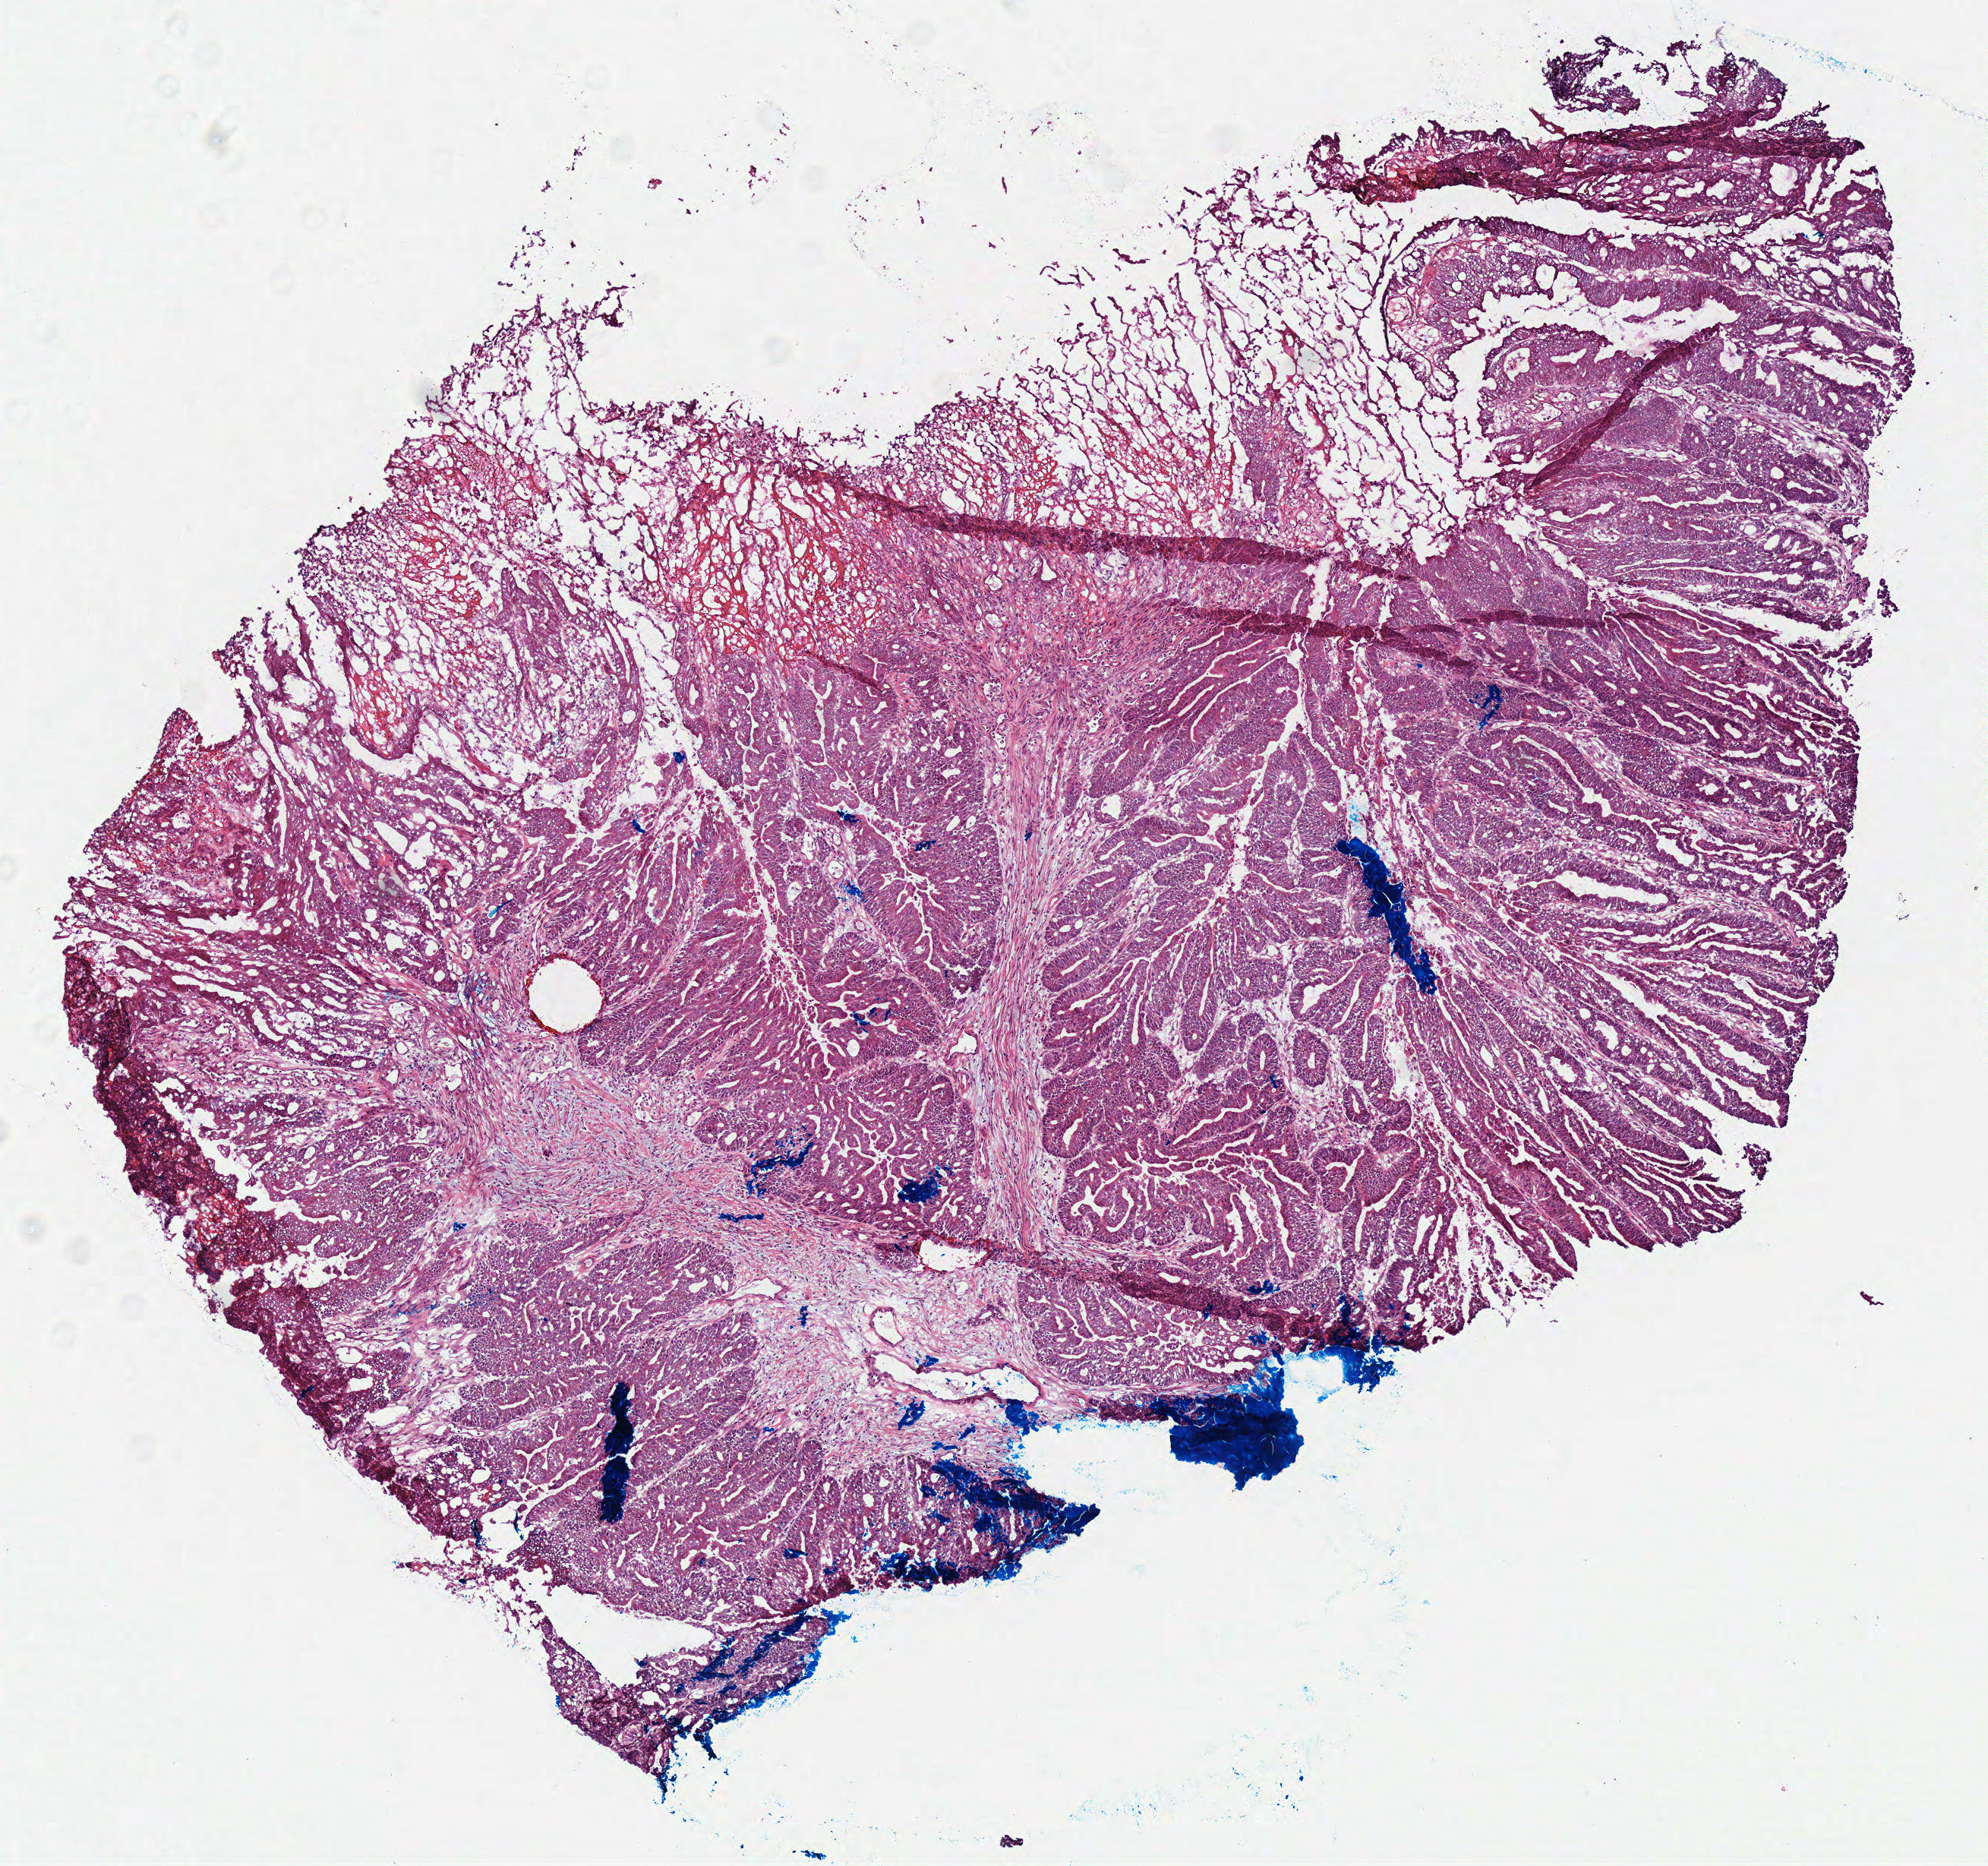
Hematoxylin and eosin (H&E) stained whole-slide image — shown as a low-resolution overview of the whole scanned area (about 5.2 x 4.8 mm, from a 40x scan); frozen section; sample: primary tumour, colon. Male patient; age at initial diagnosis 76 years. Composition of this section per pathologist review: tumour cells 85%, tumour nuclei 80%, normal cells 0%, stromal cells 15%, necrosis 0%.
AJCC pathologic stage: IIA. Histologic diagnosis: Adenocarcinoma, NOS (ascending colon).